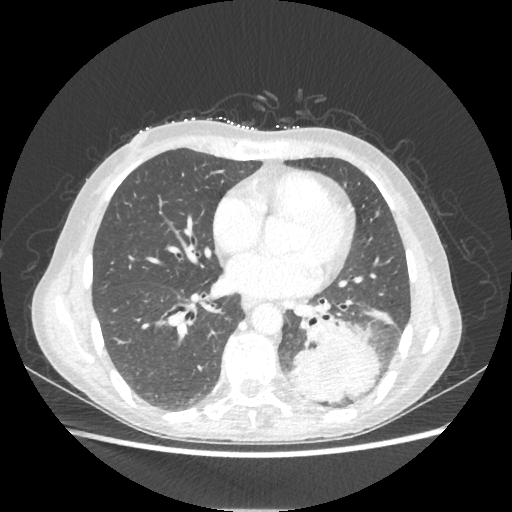
Chest CT, one axial slice; position 98 of 221 along the scan axis; 80 kVp; lung window (W 1500 / L -600 HU); 1.25 mm slice thickness; 512 × 512 image matrix, field of view 360 × 360 mm. Female patient, age 53 years. Case-level facts recorded for this patient, not image findings: clinical TNM (as recorded): T3 N0 M0.
Structures marked on this image (bounding box drawn by a radiologist):
- lung tumour (recorded histology: adenocarcinoma): bounding box (x1, y1, x2, y2) in pixels: (288, 320, 380, 402)